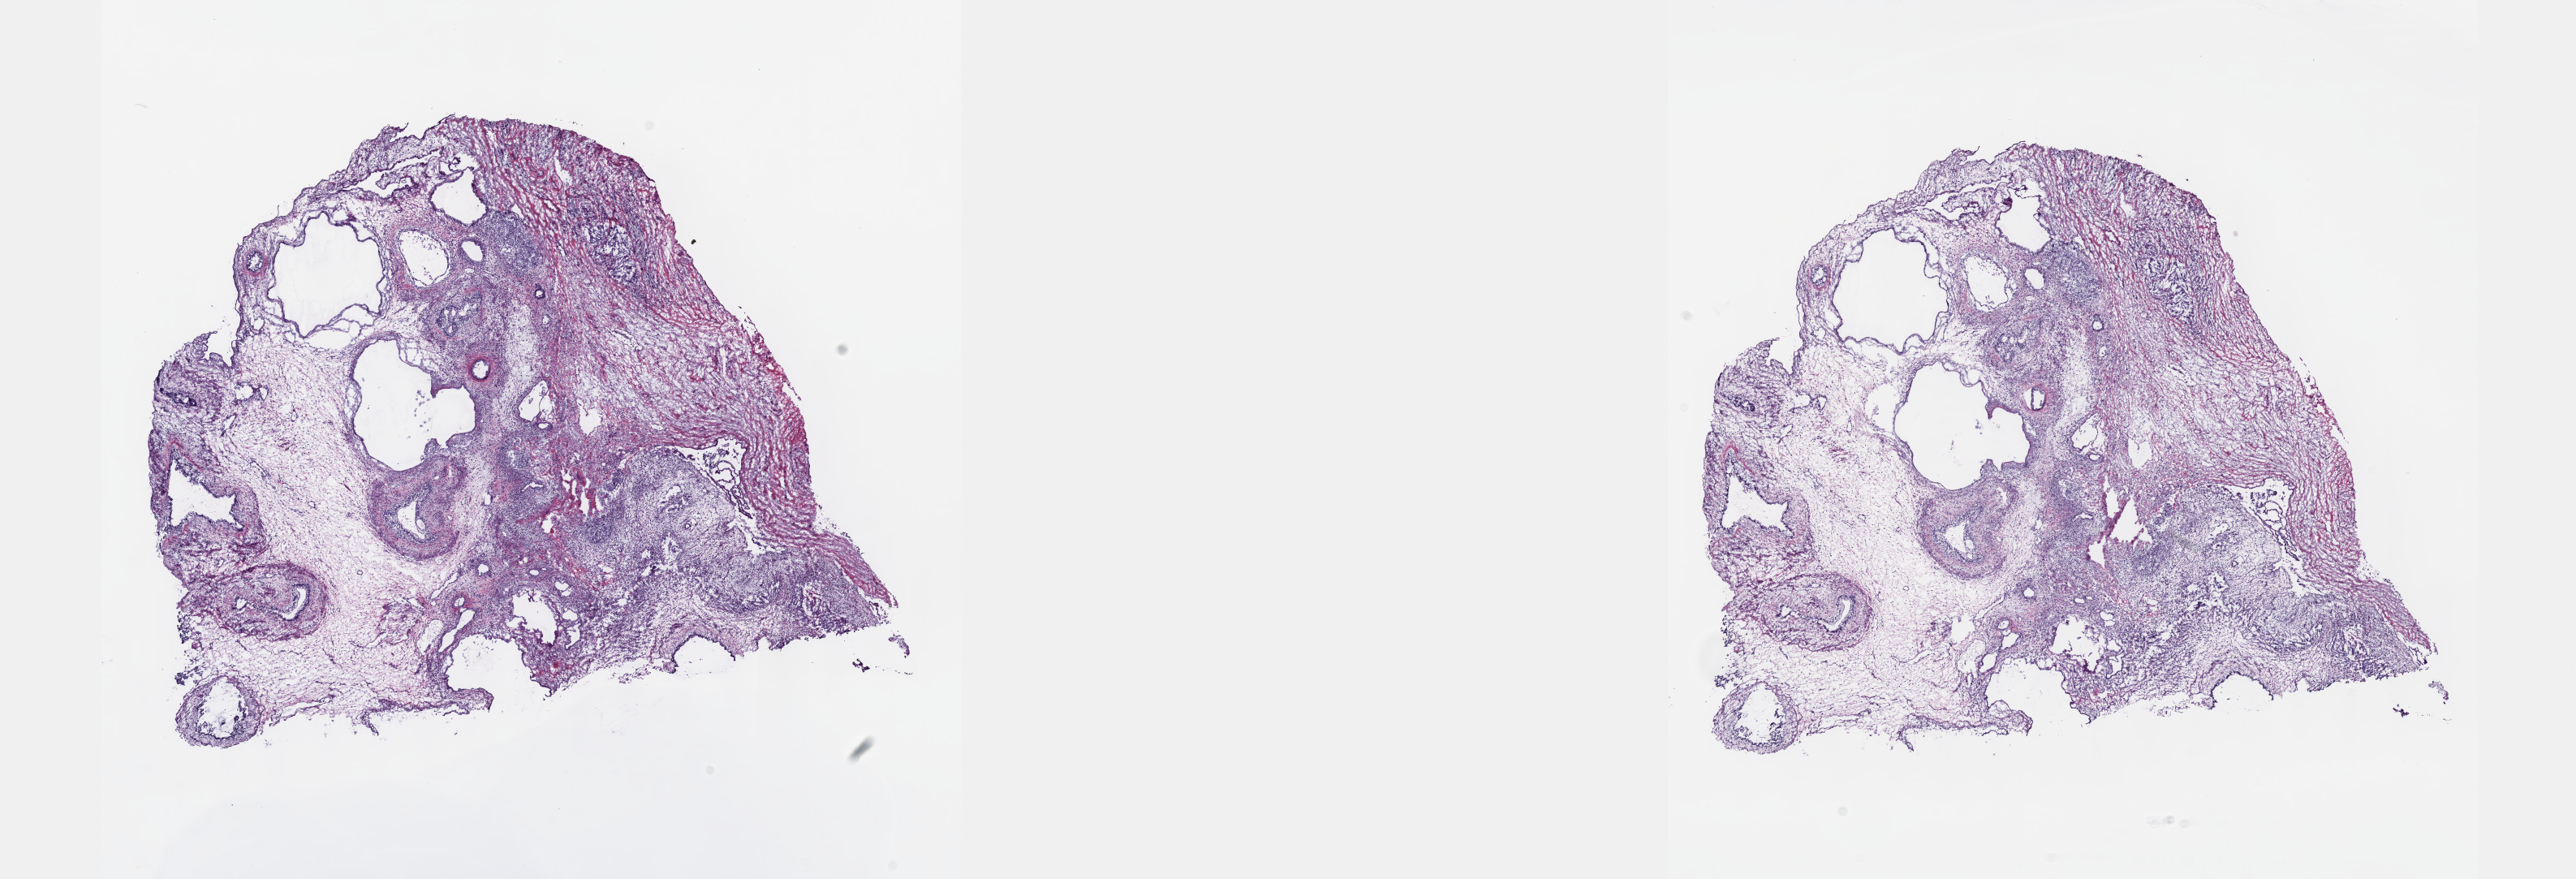
H&E whole-slide image, low-resolution overview of the scanned area, about 25.7 x 8.8 mm (slide scanned at 40x), frozen section, primary tumour sample from the testis. Male, age 33 years at initial diagnosis. Pathologist review of this section (percent, as recorded): tumour cells 90%, tumour nuclei 90%, normal cells 0%, stromal cells 10%, necrosis 0%. Infiltration values recorded for this section: lymphocyte infiltration 40%, monocyte infiltration 20%, neutrophil infiltration 20%.
* AJCC pathologic stage: IIA (6th edition)
* histologic diagnosis: Mixed germ cell tumor